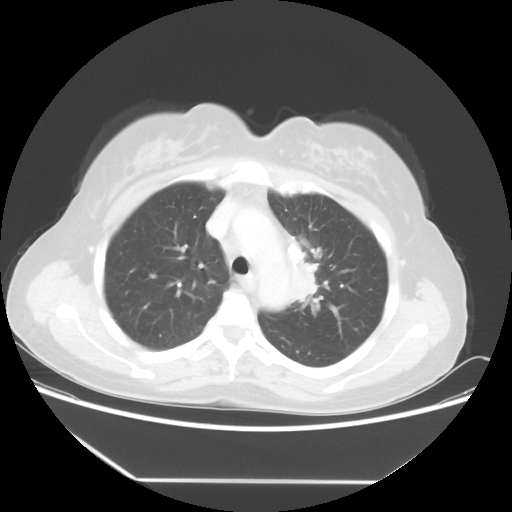
Chest CT, one axial slice. Position 38 of 52 along the scan axis. Reconstruction kernel STANDARD. Lung window (W 1500 / L -600 HU). 512 × 512 image matrix, field of view 390 × 390 mm. Patient: female, 50 years. Case-level facts recorded for this patient, not image findings: clinical TNM (as recorded): T2 N3 M0.
Structures marked on this image (rectangle marked by the reading radiologist):
- lung tumour (recorded histology: adenocarcinoma): bounding box (x1, y1, x2, y2) in pixels: (284, 227, 325, 315)